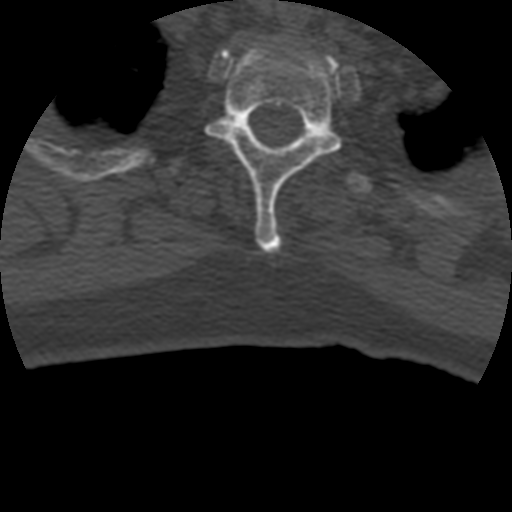
CT including the spine, one axial slice; position 367 of 399 along the scan axis; reconstruction kernel STANDARD; bone window (W 1800 / L 400 HU); 1.25 mm slice thickness; 512 × 512 image matrix, field of view 160 × 160 mm. Patient age 69 years. From the clinical record (not read from this slice): primary cancer: prostate.
Structures marked on this image (semi-automatic segmentation, software-assisted and operator-edited):
- T1 vertebra: bounding box (x1, y1, x2, y2) in pixels: (328, 56, 337, 73)
- T2 vertebra: (206, 40, 343, 254)
- T3 vertebra: (169, 157, 372, 198)